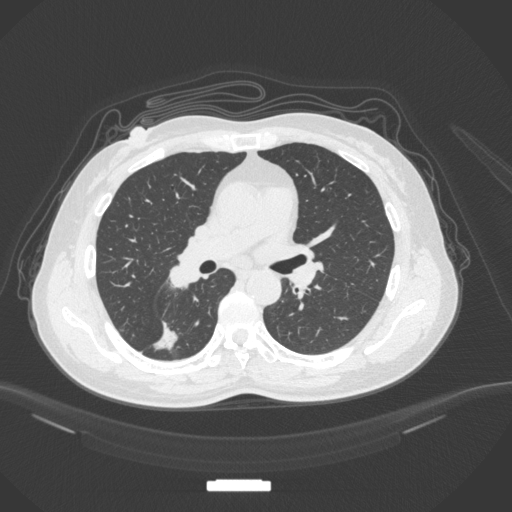
Chest CT, one axial slice. Position 173 of 352 along the scan axis. Reconstruction kernel B31f. 120 kVp. Lung window (W 1500 / L -600 HU). 1 mm slice thickness. 512 × 512 image matrix, field of view 400 × 400 mm. Female patient, age 55 years. Case-level facts recorded for this patient, not image findings: clinical TNM (as recorded): T1c N1 M0.
Outlined on this slice (bounding box drawn by a radiologist):
- lung tumour (recorded histology: adenocarcinoma): box from (x=143, y=313) to (x=183, y=353) px